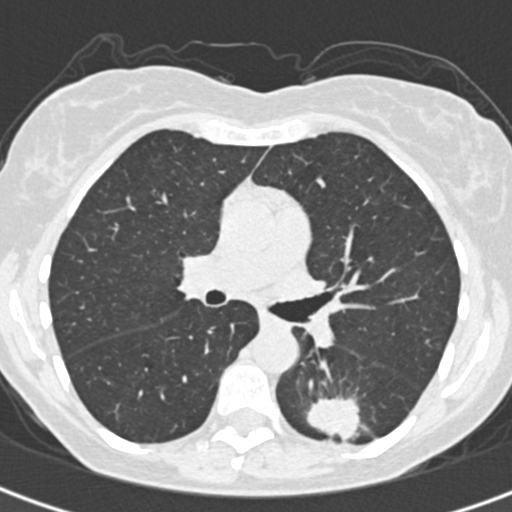
Low-dose screening chest CT, one axial slice. Position 199 of 328 along the scan axis. Reconstruction kernel B30f. Lung window (W 1500 / L -600 HU). 512 × 512 image matrix, field of view 284 × 284 mm.
Structures marked on this image (manually delineated by an expert):
- lesion 1 (tumor, lower lobe of left lung): bounding box (x1, y1, x2, y2) in pixels: (307, 397, 361, 441)